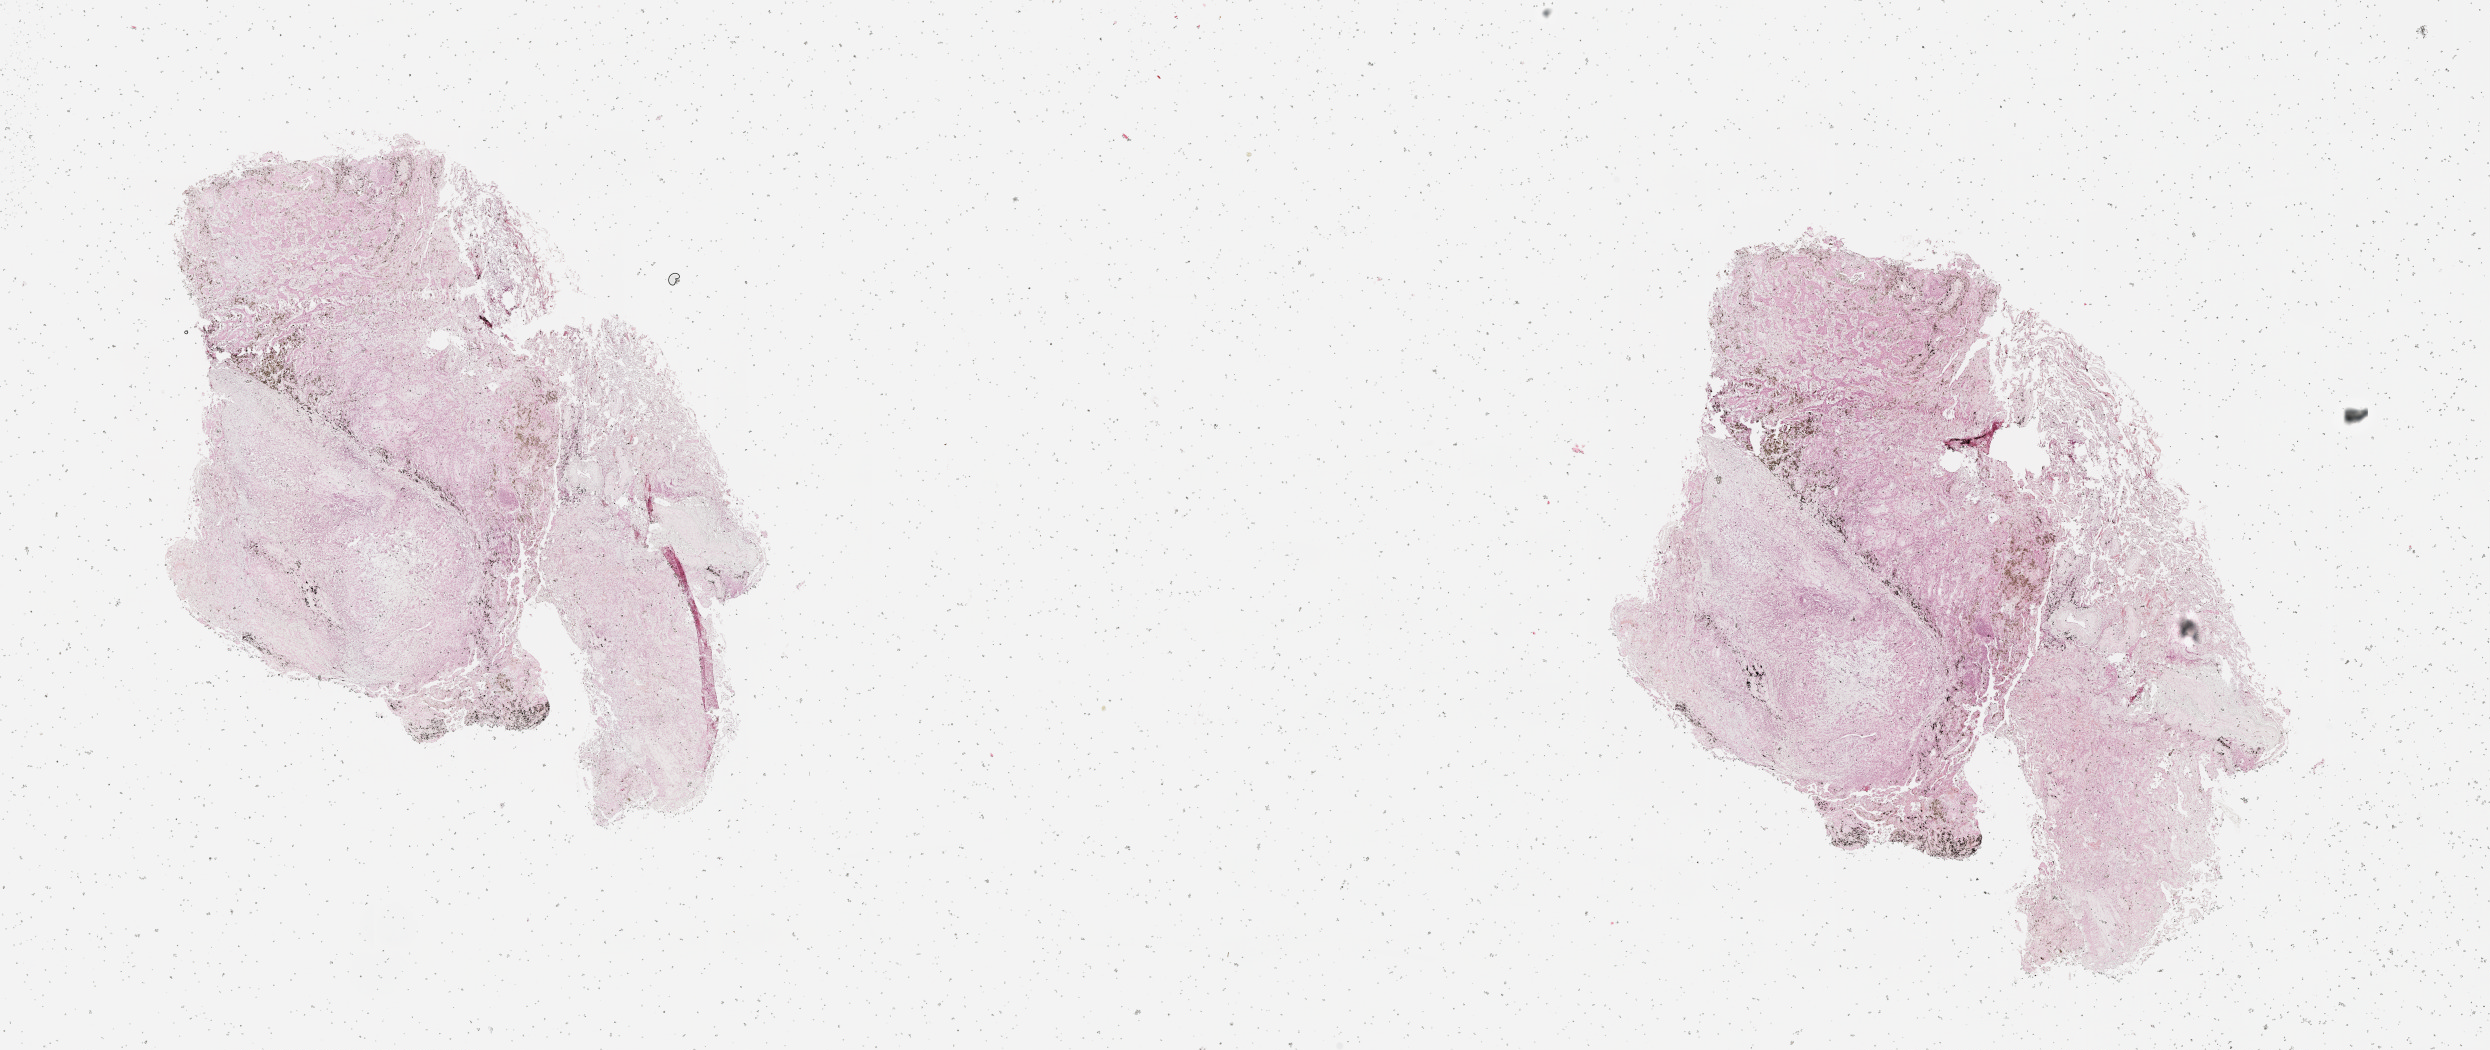
Hematoxylin and eosin (H&E) stained whole-slide image, shown as a low-resolution overview of the whole scanned area (about 20.0 x 8.5 mm, slide scanned at 20x); lung, tissue type not recorded.
- patient diagnosis (cohort enrolment): squamous cell carcinoma (lung)